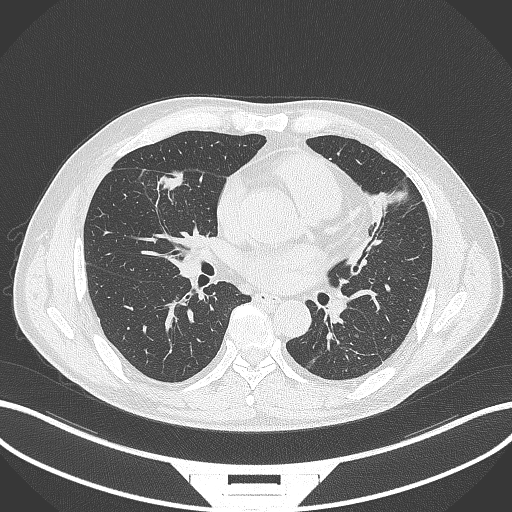
Chest CT, one axial slice; position 150 of 399 along the scan axis; 120 kVp; lung window (W 1500 / L -600 HU); 1 mm slice thickness; 512 × 512 image matrix, field of view 400 × 400 mm. Male patient, age 59 years. Case-level facts recorded for this patient, not image findings: clinical TNM (as recorded): T2a N1 M0.
Annotated regions visible in this slice (rectangle marked by the reading radiologist):
- lung tumour (recorded histology: adenocarcinoma): bounding box [x1, y1, x2, y2] px = [159, 165, 189, 196]